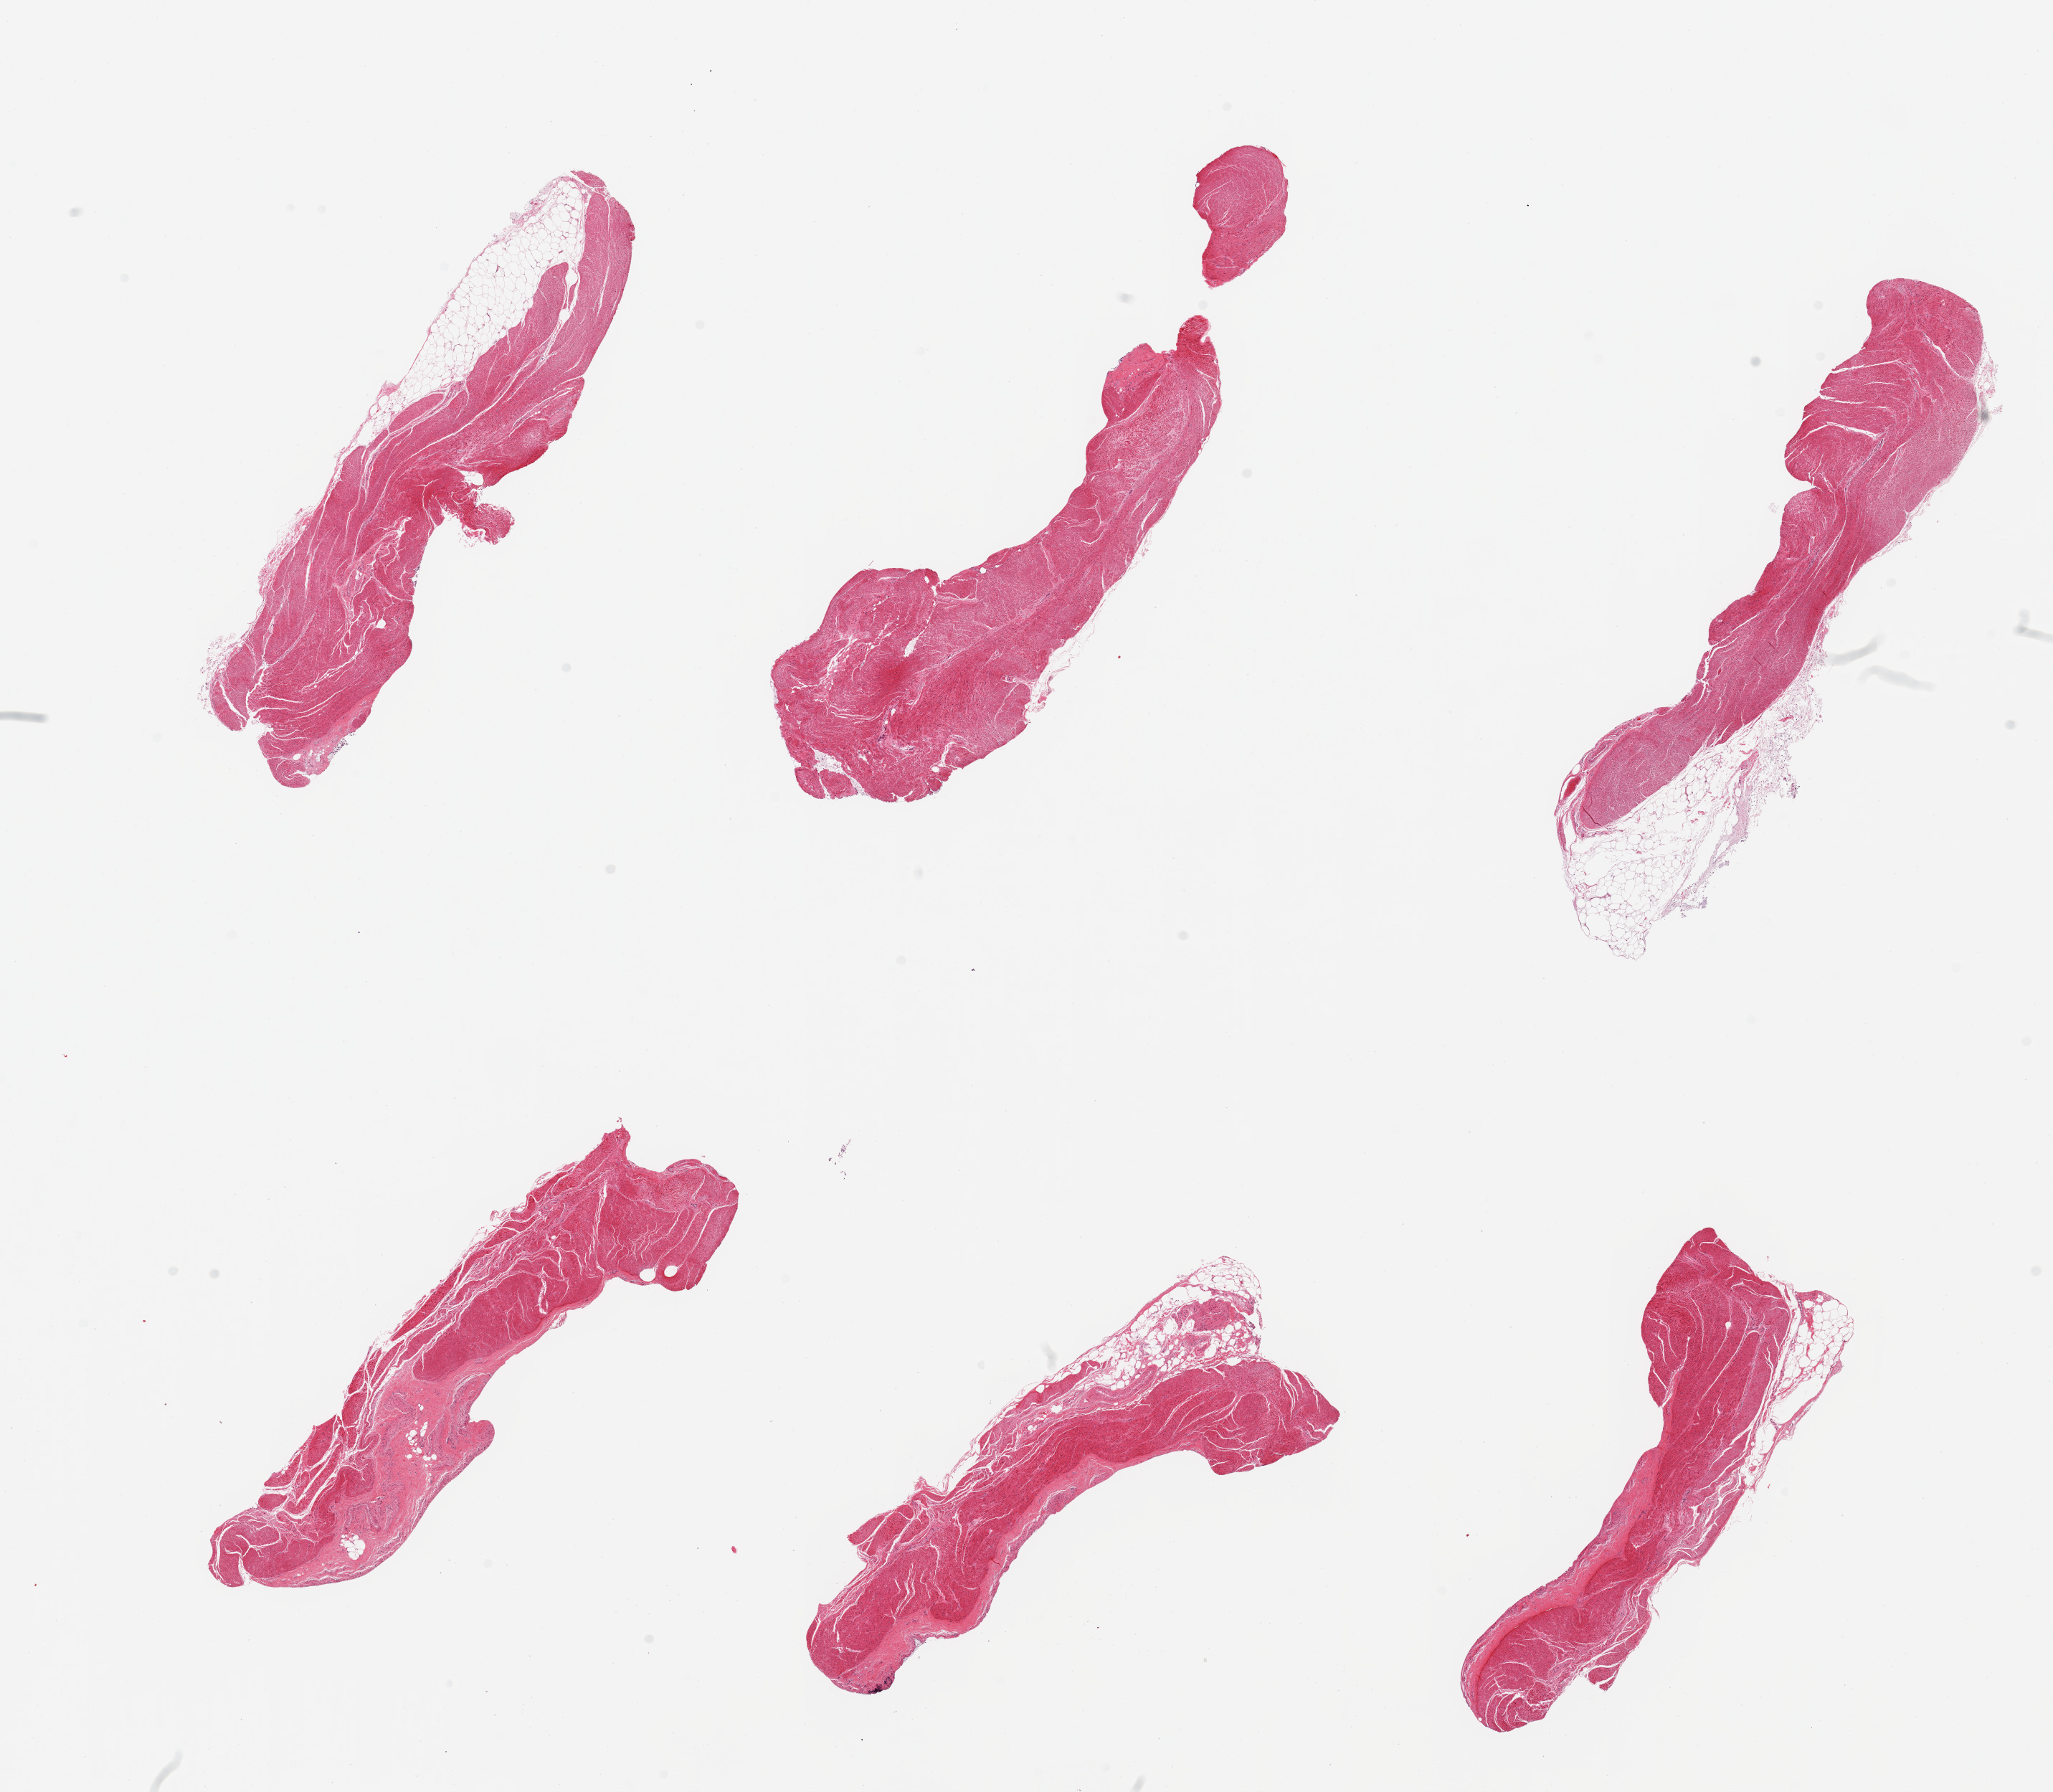
Digitized hematoxylin and eosin (H&E)-stained section, low-resolution overview of the scanned area, about 22.6 x 19.8 mm. PAXgene-fixed paraffin-embedded (PFPE) section. Sampled site (target tissue): sigmoid colon. Donor tissue sample. Male donor.
Reviewer comment on this tissue sample: 6 pieces; muscularis, several pieces with up to 20% attached fat.